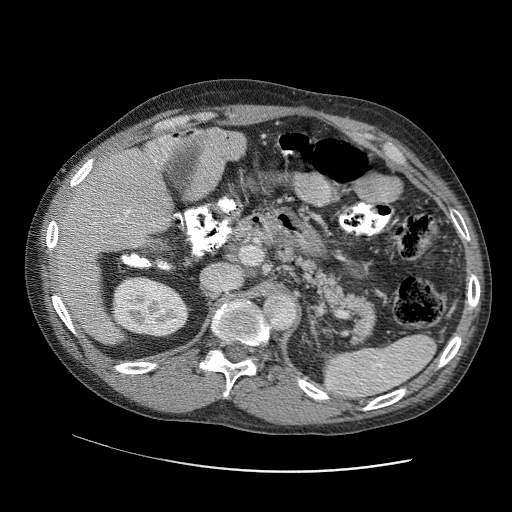
Contrast-enhanced abdominal CT (liver protocol), one axial slice. Slice 60 of 109 in the series (ordered by position). Reconstruction kernel STANDARD. Soft-tissue window (W 400 / L 40 HU). 2.5 mm slice thickness. 512 × 512 image matrix, field of view 400 × 400 mm. Case-level facts recorded for this patient, not image findings: diagnosis: hepatocellular carcinoma (patient treated with transarterial chemoembolisation; whether this scan precedes or follows treatment is not stated here); TNM stage (as recorded): Stage-IIIC; Child-Pugh class: B; tumour nodularity: uninodular.
Structures marked on this image (semi-automatic segmentation, software-assisted and operator-edited):
- liver parenchyma outside the tumour (the mass and vessels are separate outlines, so this box may not span the whole liver): bounding box <52,129,246,322> (left, top, right, bottom; pixels)
- liver vessels: <61,130,244,281>